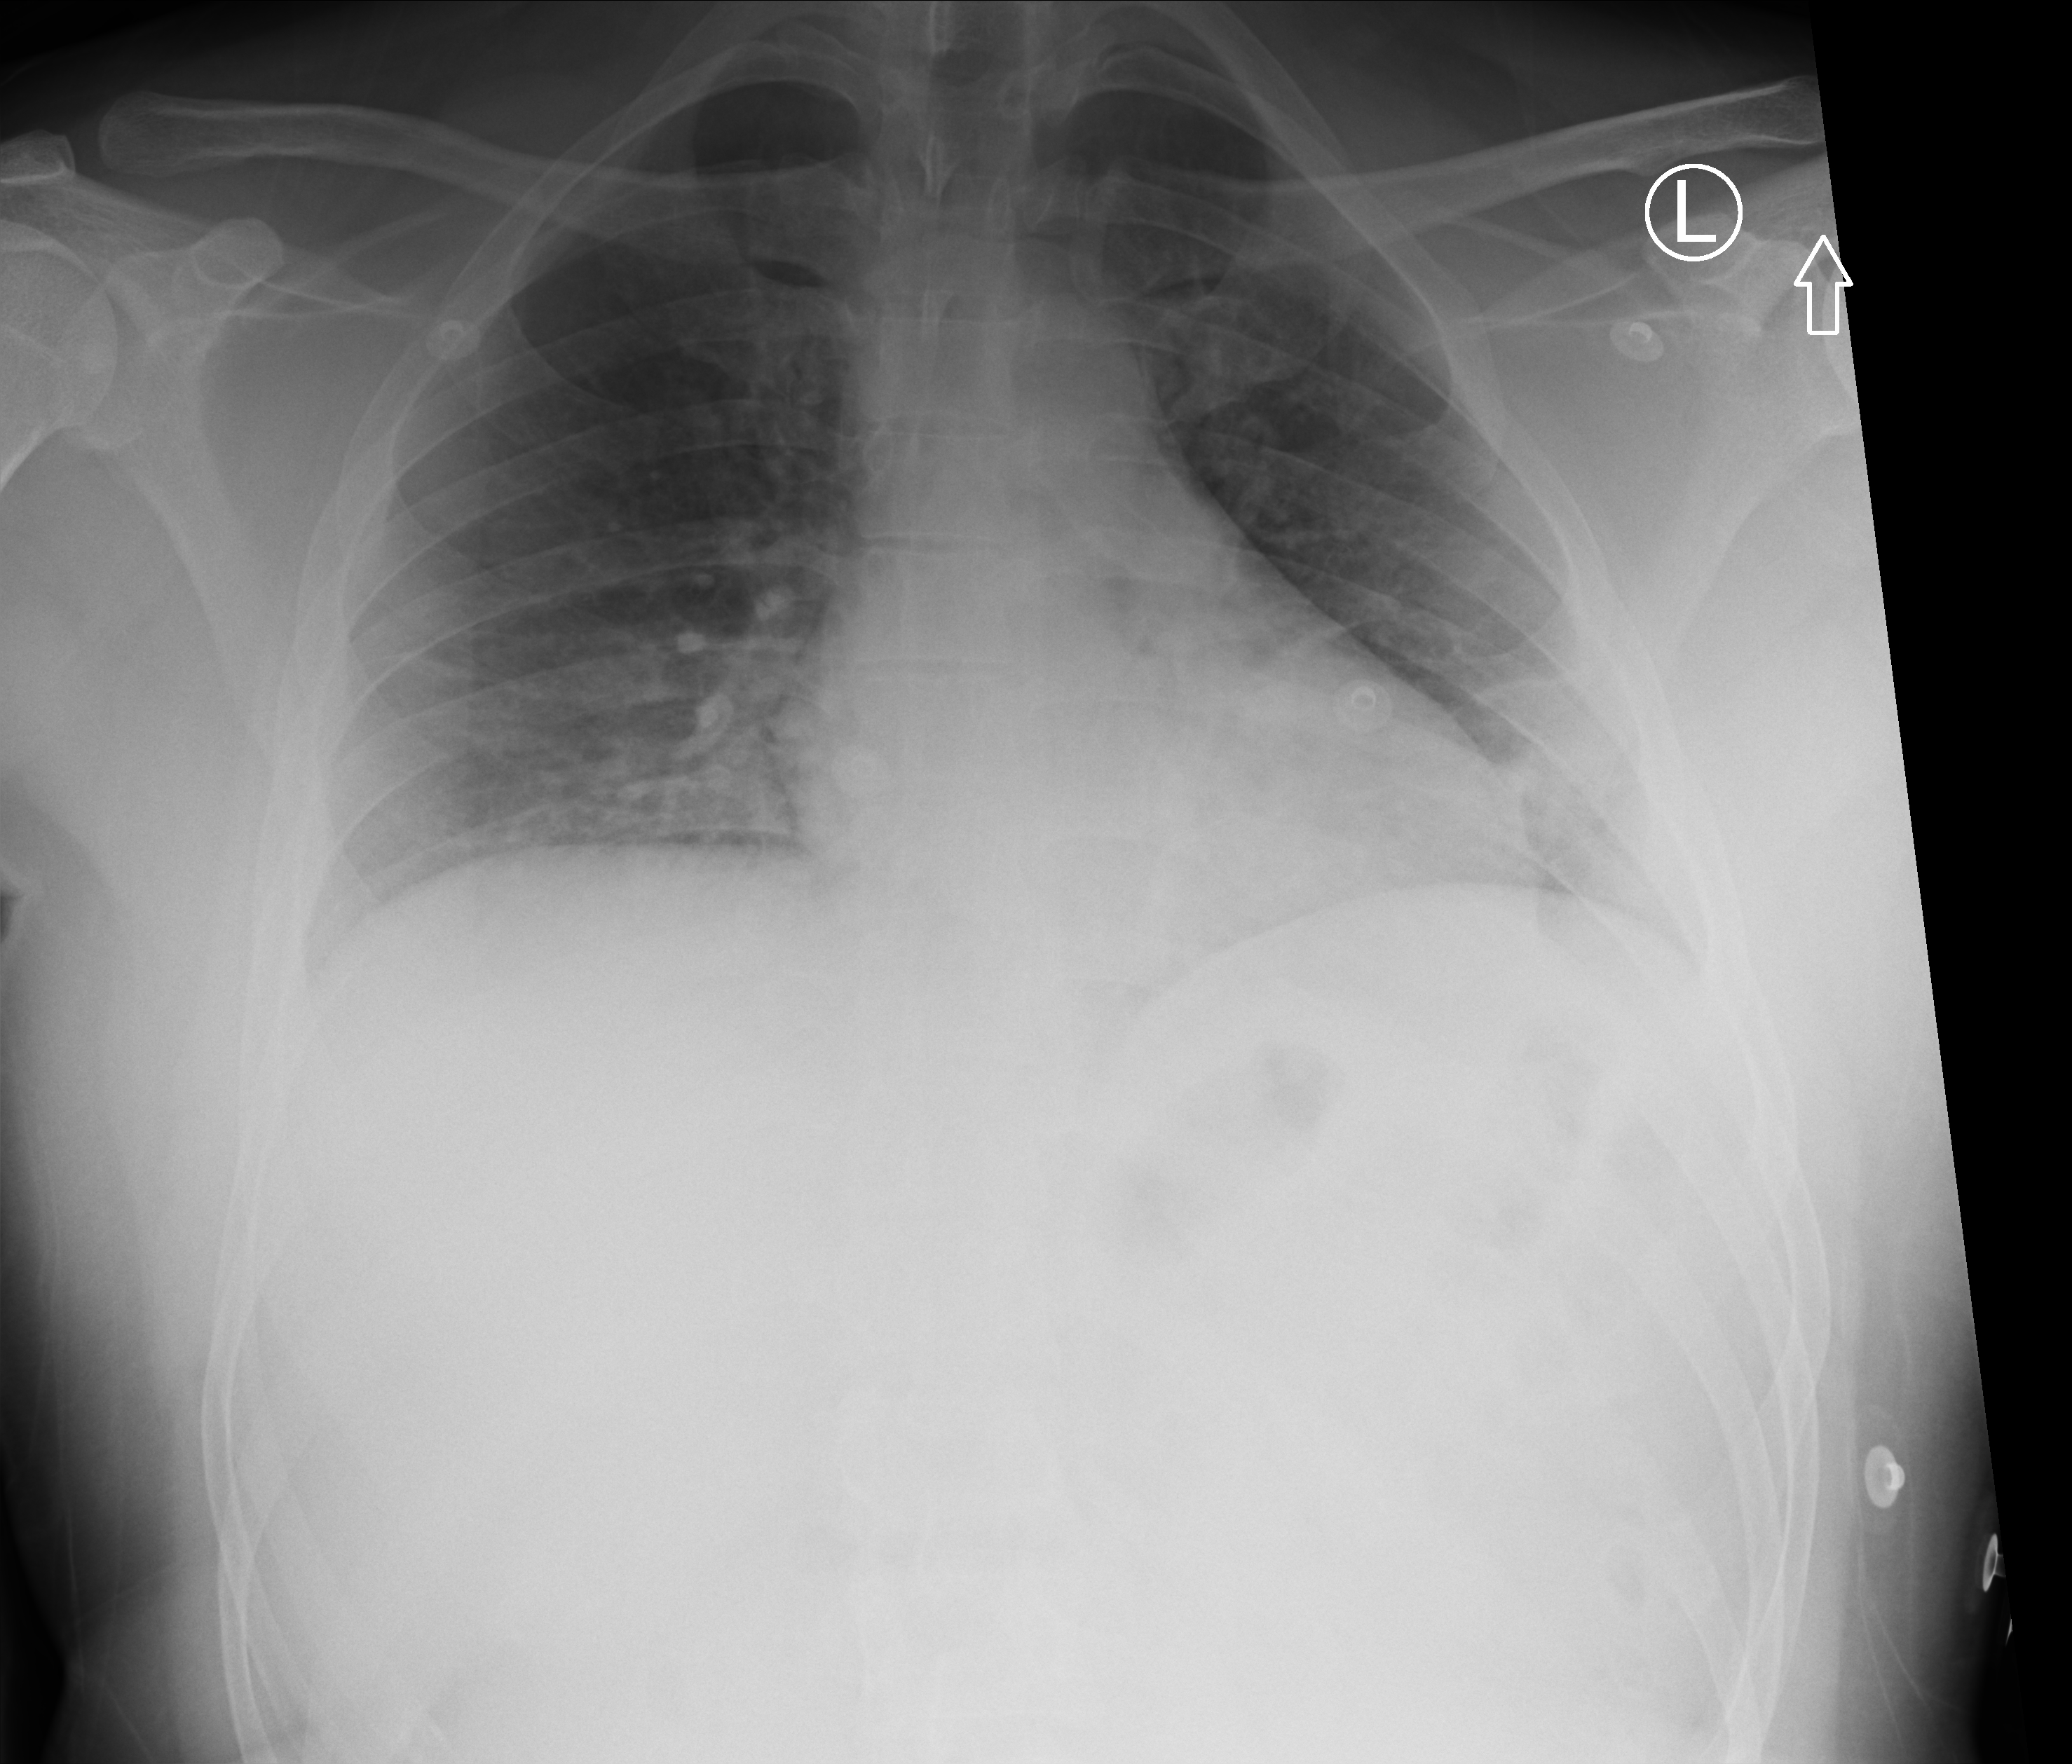
Portable chest radiograph; anteroposterior (AP) projection. Male patient hospitalised with COVID-19, age 18–59 years.
From the hospital-stay record, not from the radiograph (when in the stay this image was taken is not recorded): length of hospital stay: 8 days; admitted to intensive care during this hospital stay: no.